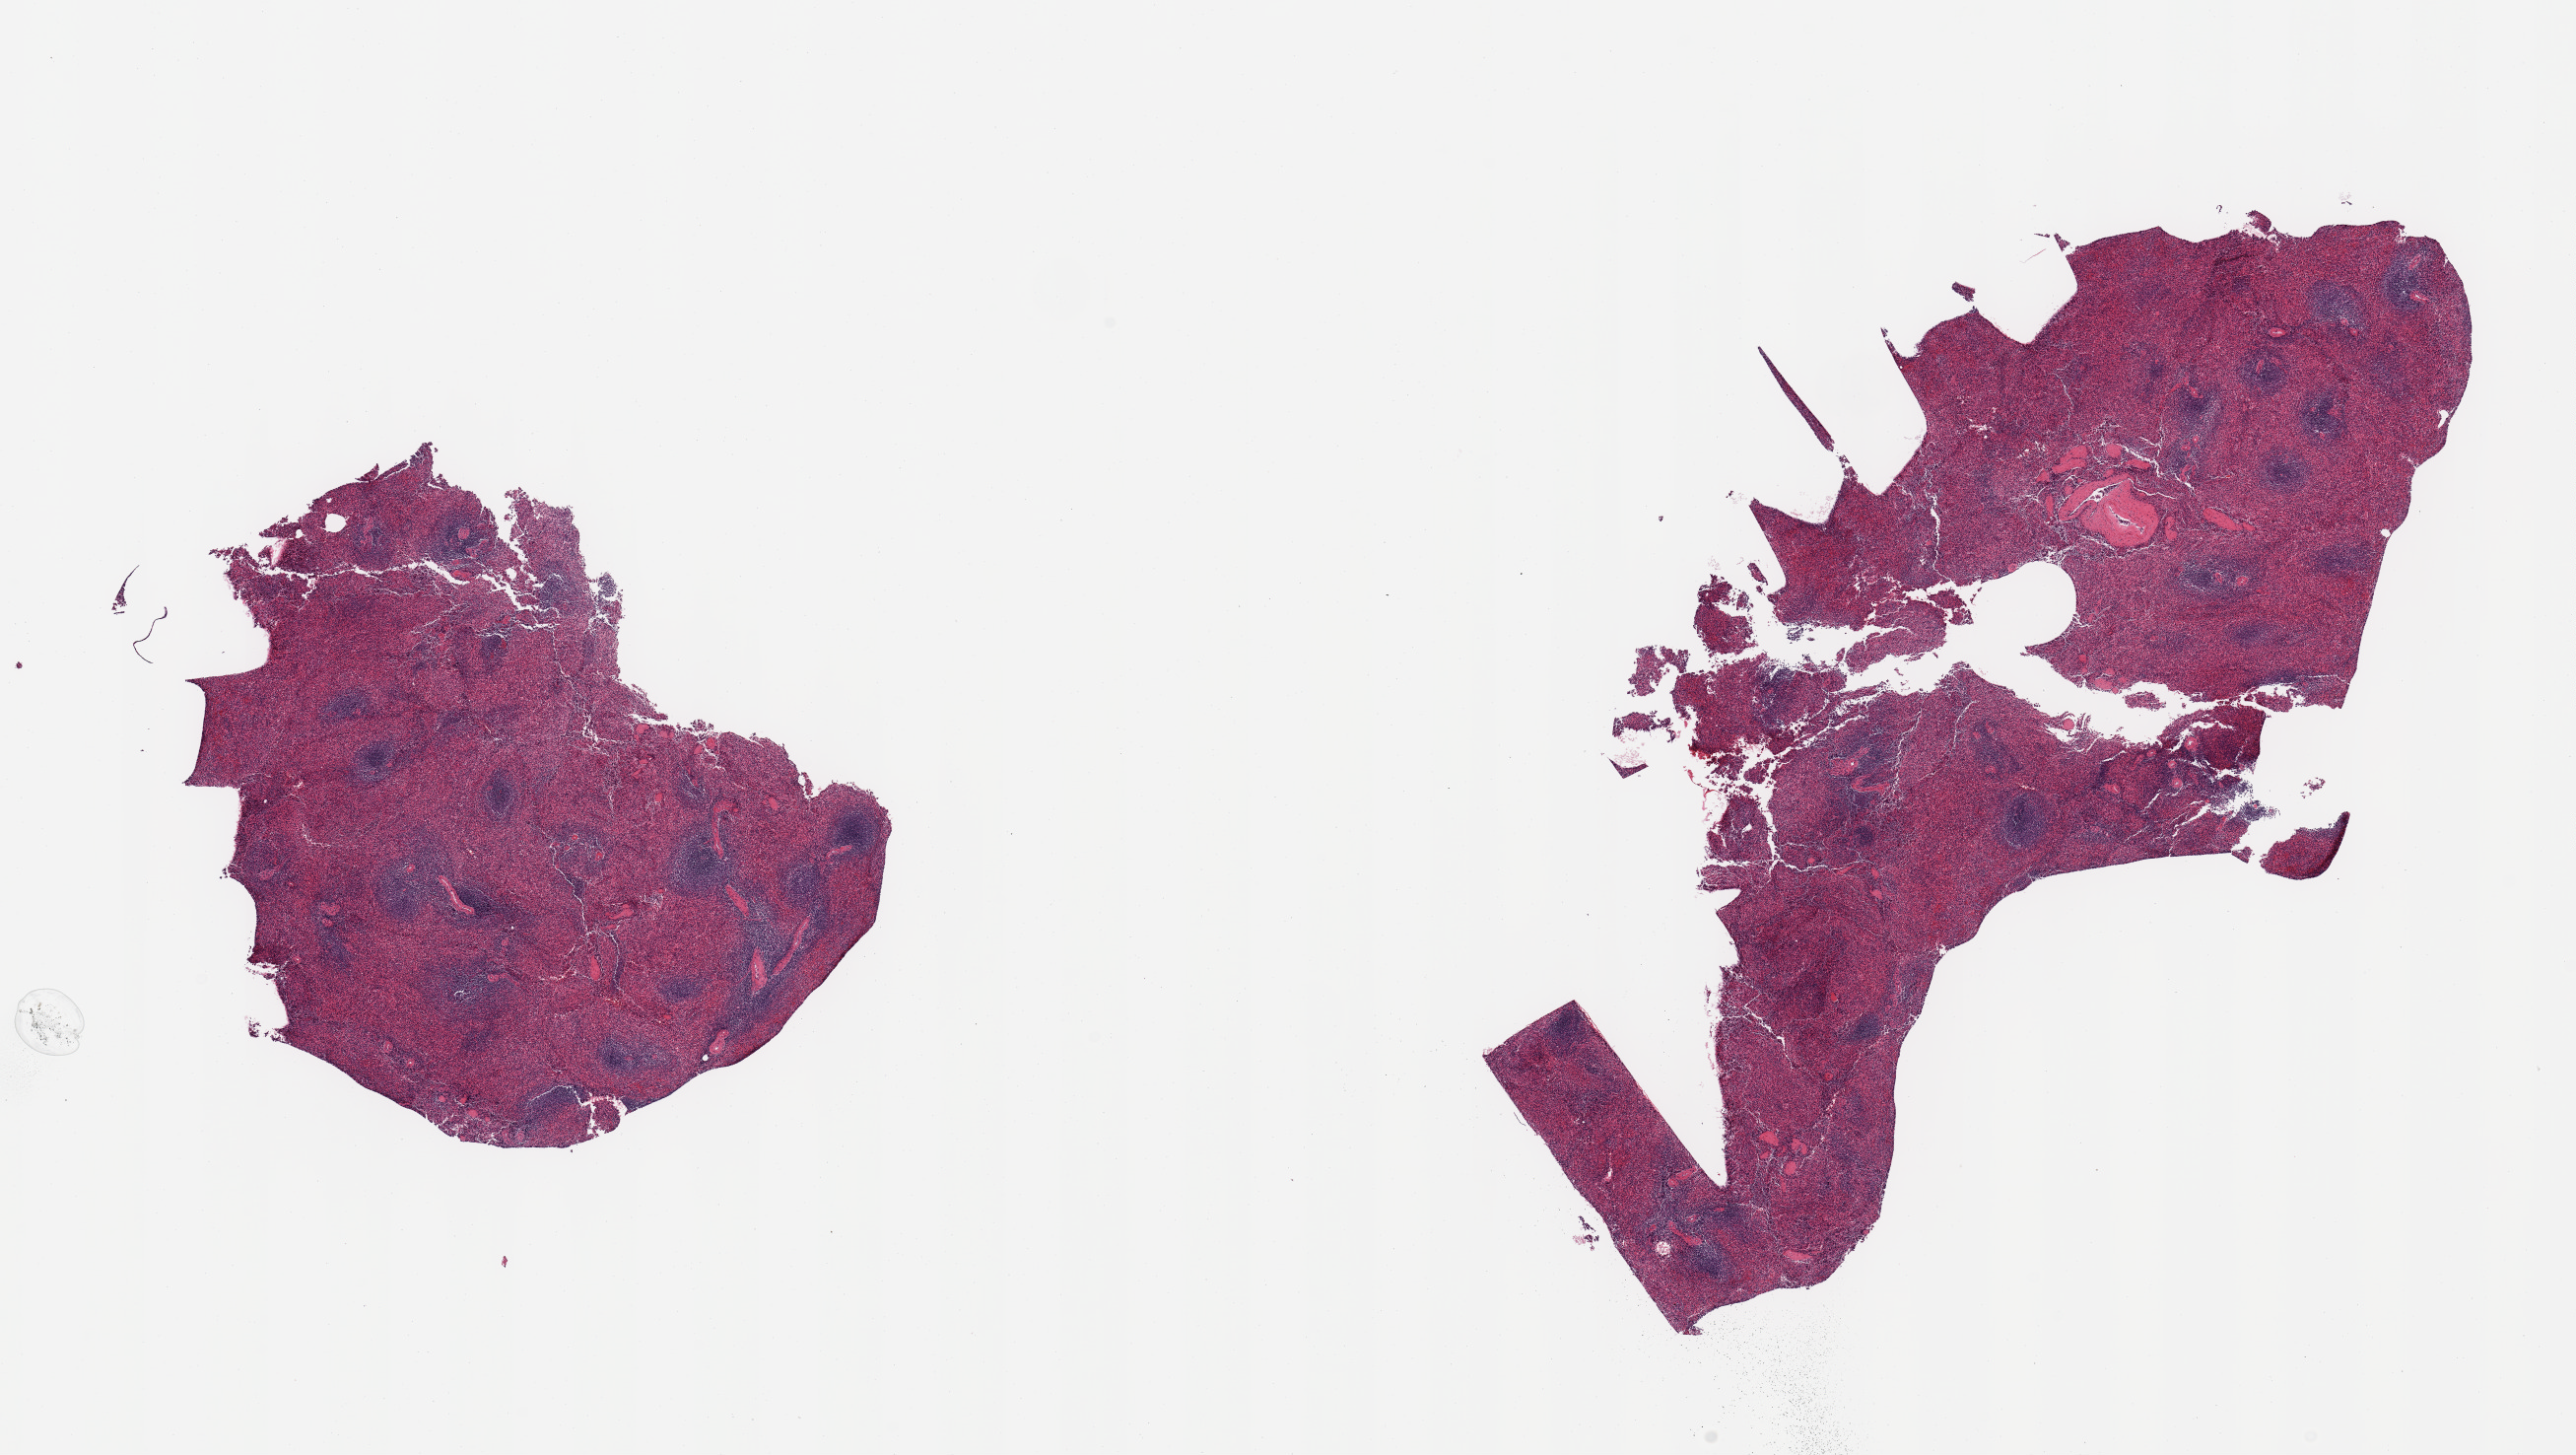
H&E whole-slide image, brightfield — shown as a low-resolution overview of the whole scanned area (about 20.7 x 11.7 mm); PAXgene-fixed, paraffin-embedded tissue; target tissue: spleen; donor tissue sample. Donor sex: female.
• review note (as recorded): 2 pieces